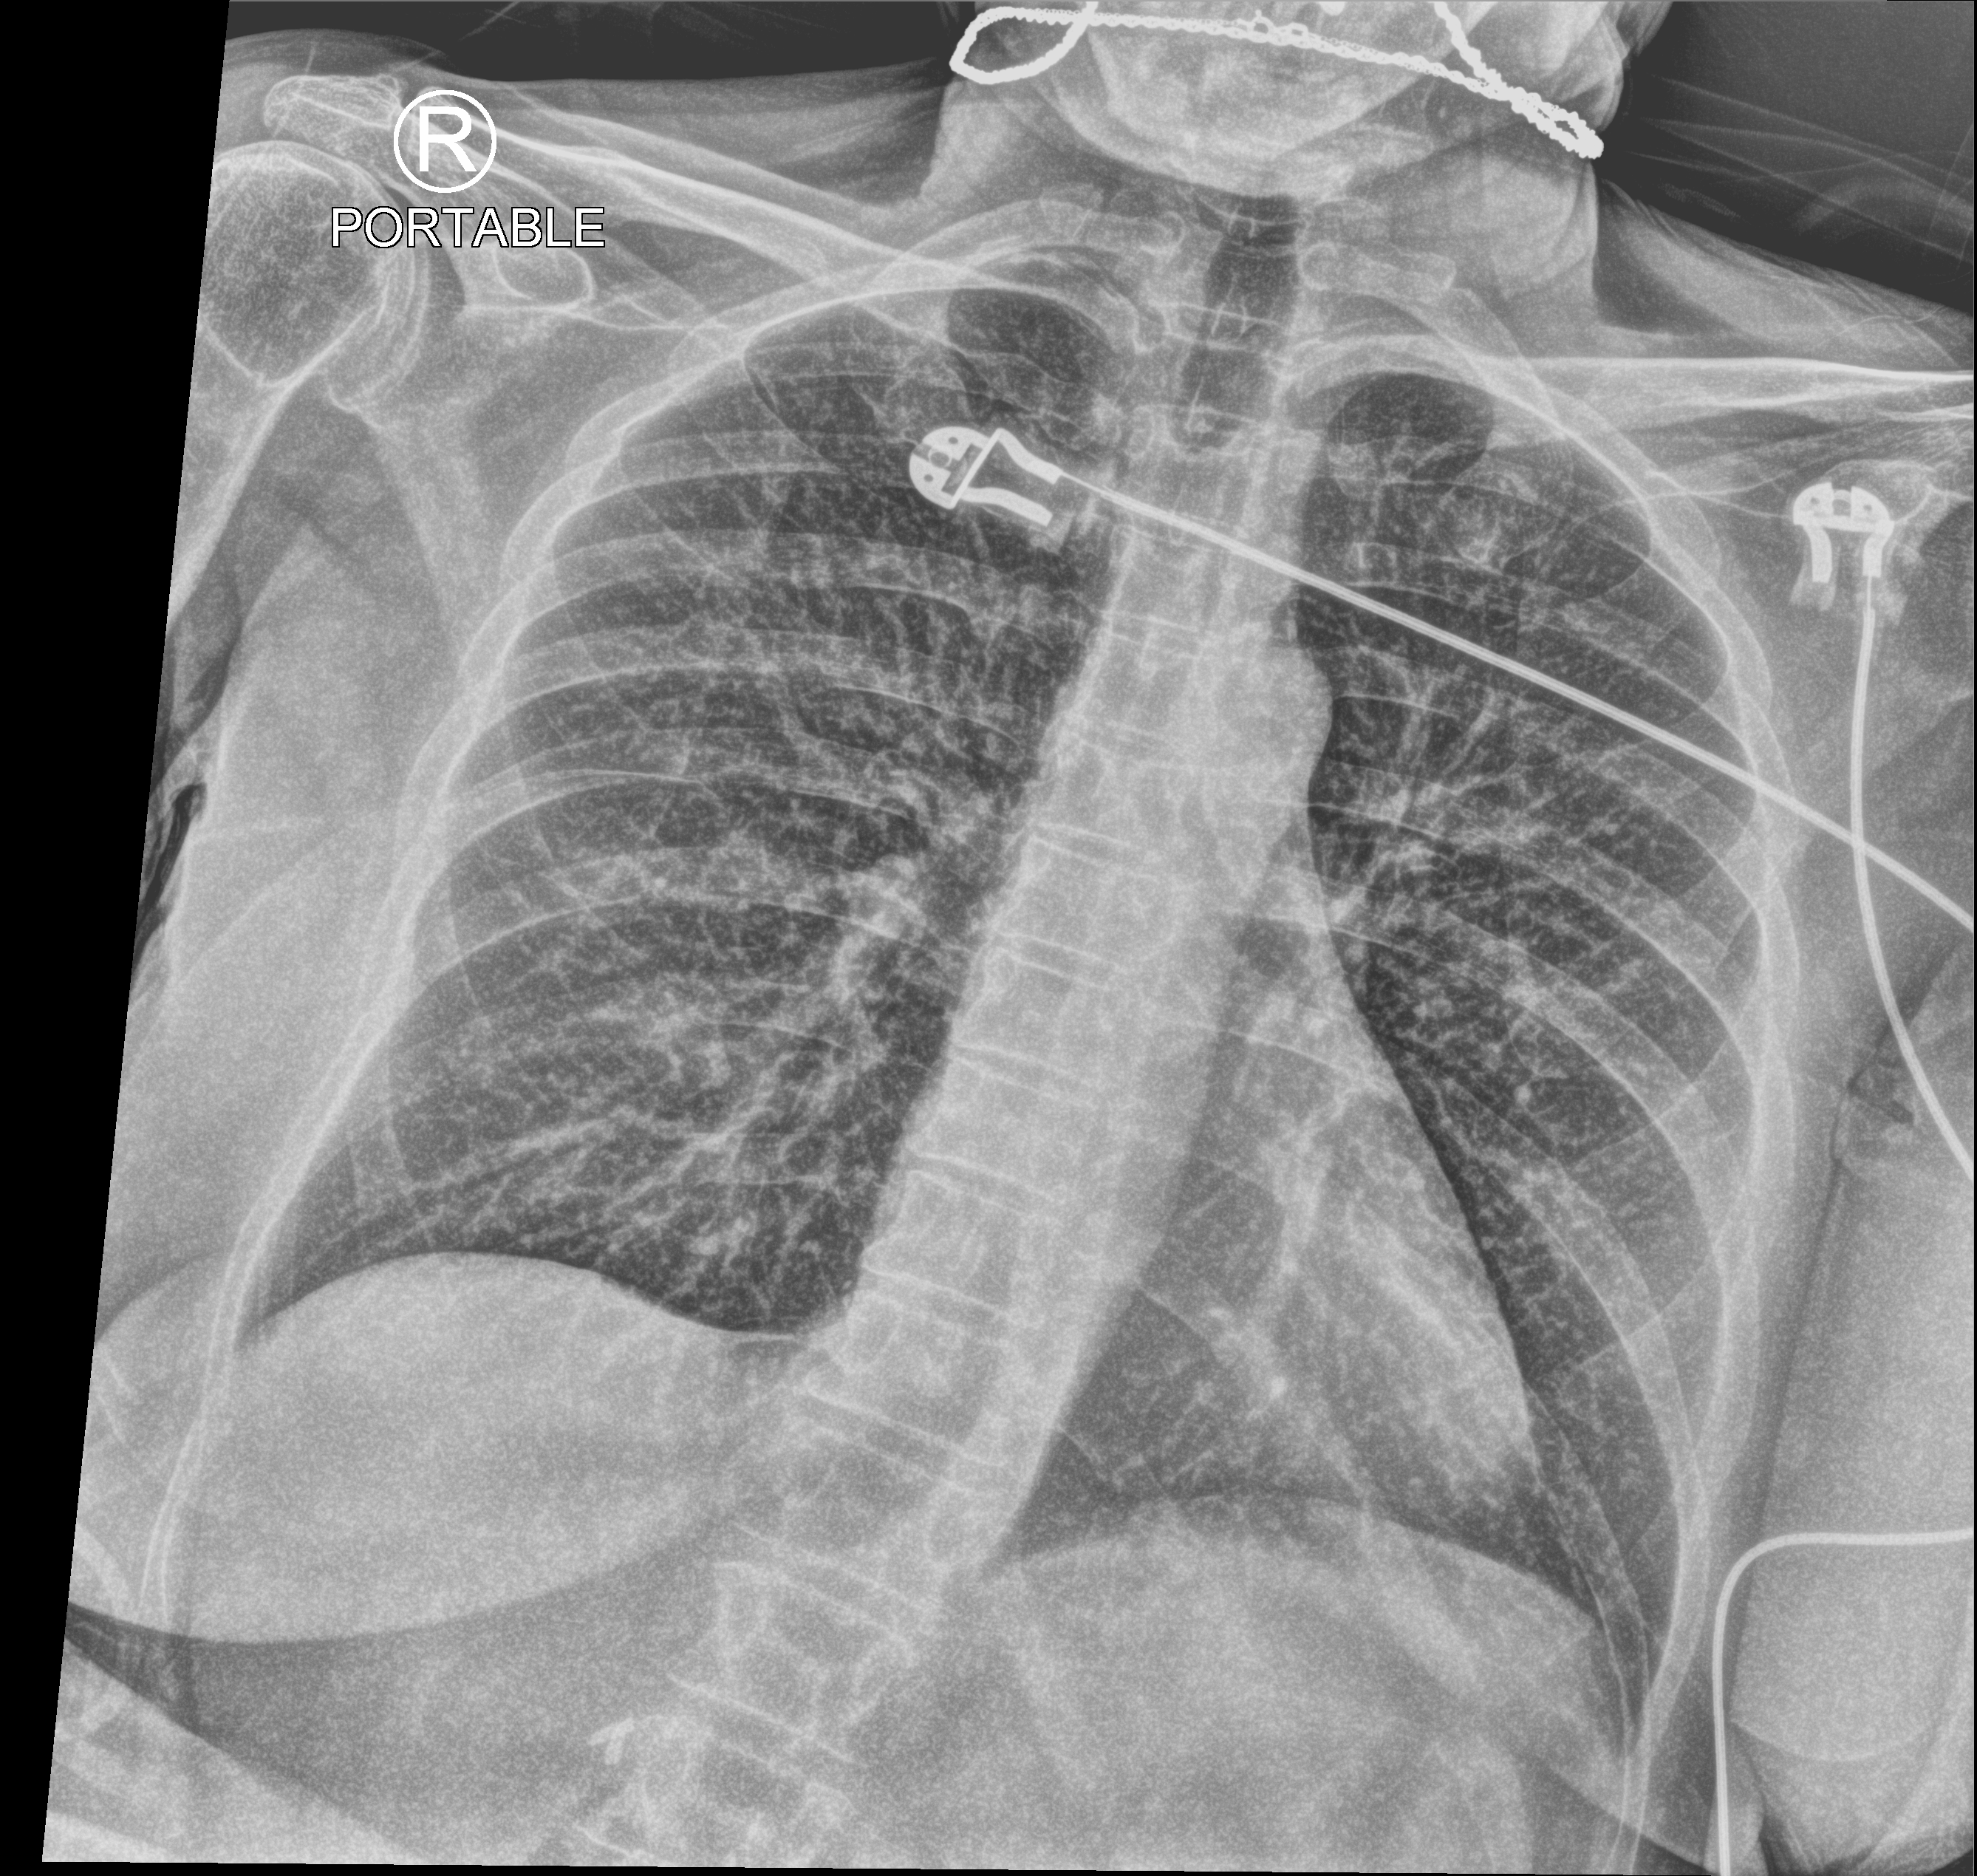
Chest X-ray (portable); anteroposterior (AP) projection. Female patient hospitalised with COVID-19, age 60–74 years.
Admission-level facts for this patient (not findings on this image; timing relative to this image not recorded):
- admitted to intensive care during this hospital stay: no